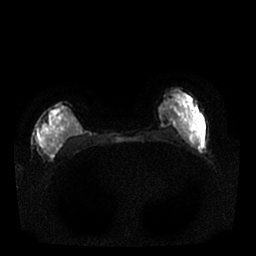
Breast MRI, one axial slice. Slice 10 of 25 in the series (ordered by position). Diffusion-weighted series; image 2 of 4 stored at this slice position (different b-values; order by instance number). 1.5 T. 256 × 256 image matrix, field of view 340 × 340 mm. Female patient.
Structures marked on this image (outlined manually by an expert reader):
- tumour on diffusion-weighted imaging: bounding box [x1, y1, x2, y2] px = [39, 108, 64, 156]